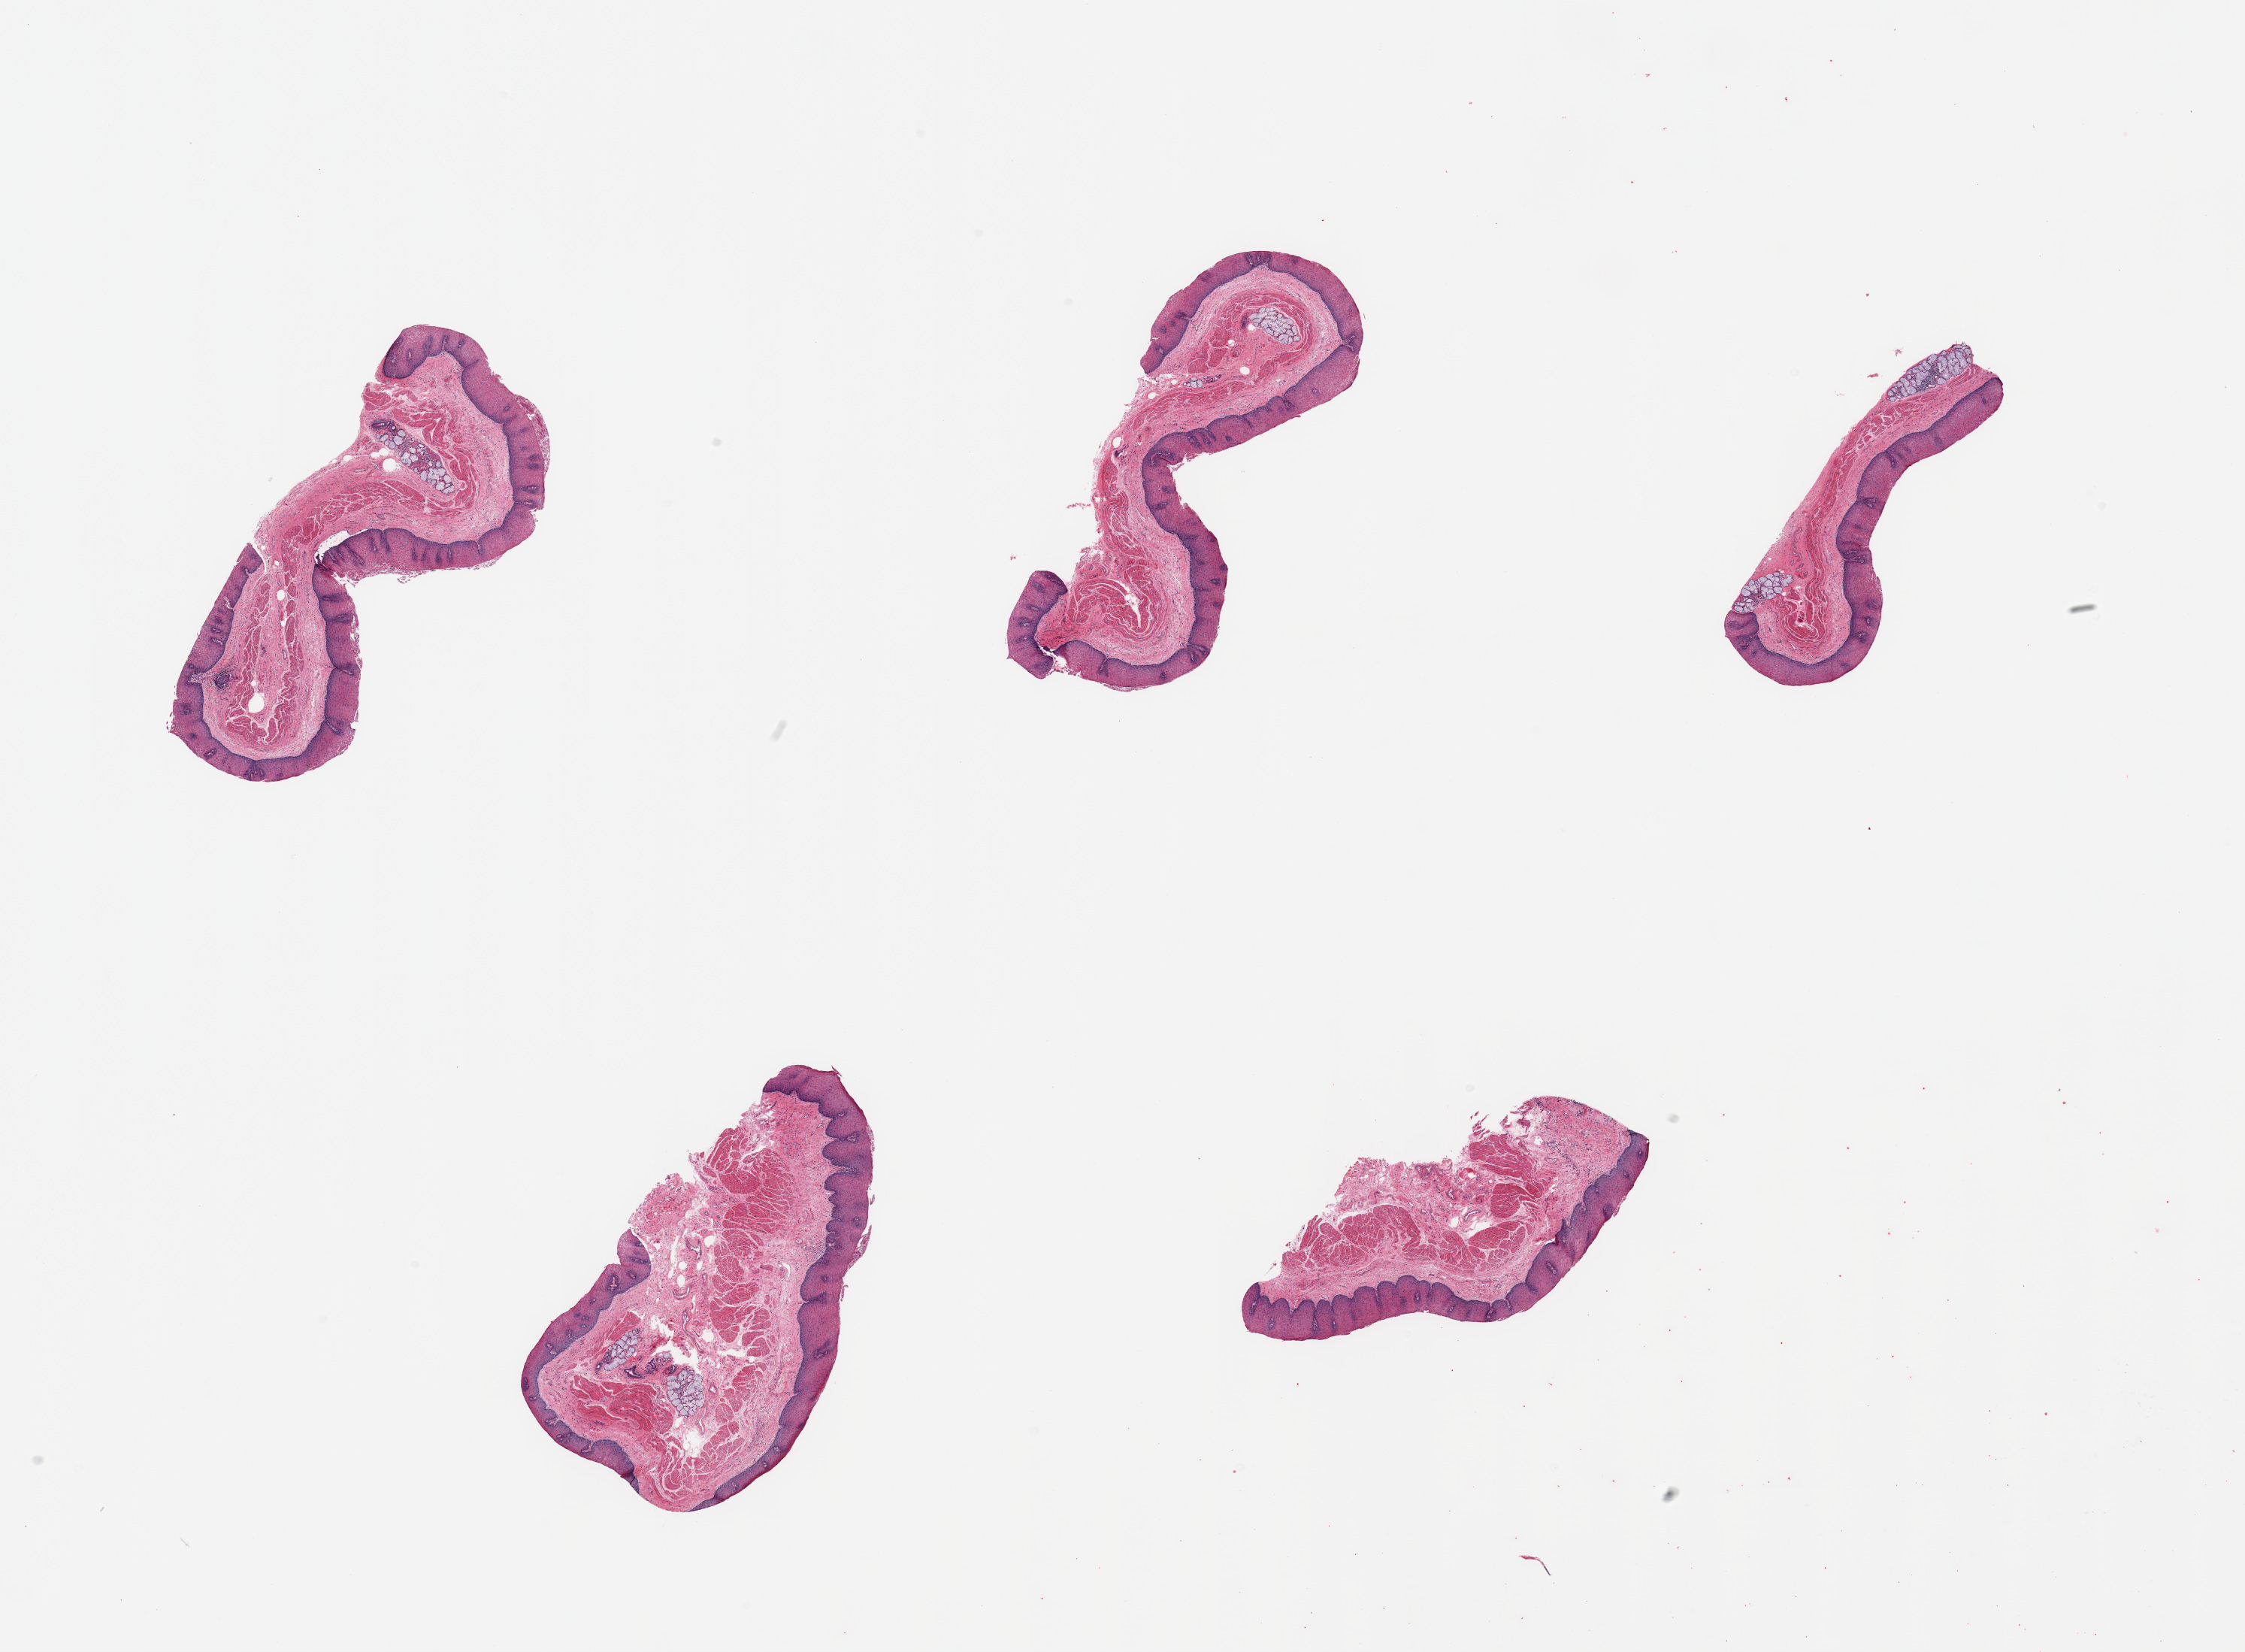
Digitized hematoxylin and eosin (H&E)-stained section, a low-resolution overview of the entire scanned area, about 23.6 x 17.4 mm (from a 20x scan). PAXgene-fixed paraffin-embedded (PFPE) section. Section of esophageal mucous membrane (target tissue). Donor tissue sample. Male donor.
Pathologist's review note for this sample: 5 pieces; squamous mucosa and submucosal glands in 4 of 5 pieces; squamous epithelium ~0.35mm thick.